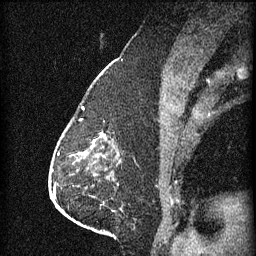
Breast MRI (dynamic contrast-enhanced), one sagittal slice; slice 30 of 60 in the series (ordered by position); 3 images stored at this slice position (order not interpretable as contrast timing); 1.5 T; TE 4.2 ms, TR 11 ms; 1.5 mm slice thickness; 256 × 256 image matrix. Patient: female, 63 years.
Annotated regions visible in this slice (semi-automatic segmentation, software-assisted and operator-edited):
- analysis volume of interest (the breast-tissue region the enhancement analysis was run in; not a lesion): bounding box <86,132,119,153> (left, top, right, bottom; pixels)
- tumour enhancement mask (voxels above the 70 % enhancement threshold inside the analysis volume of interest): <102,134,105,139>